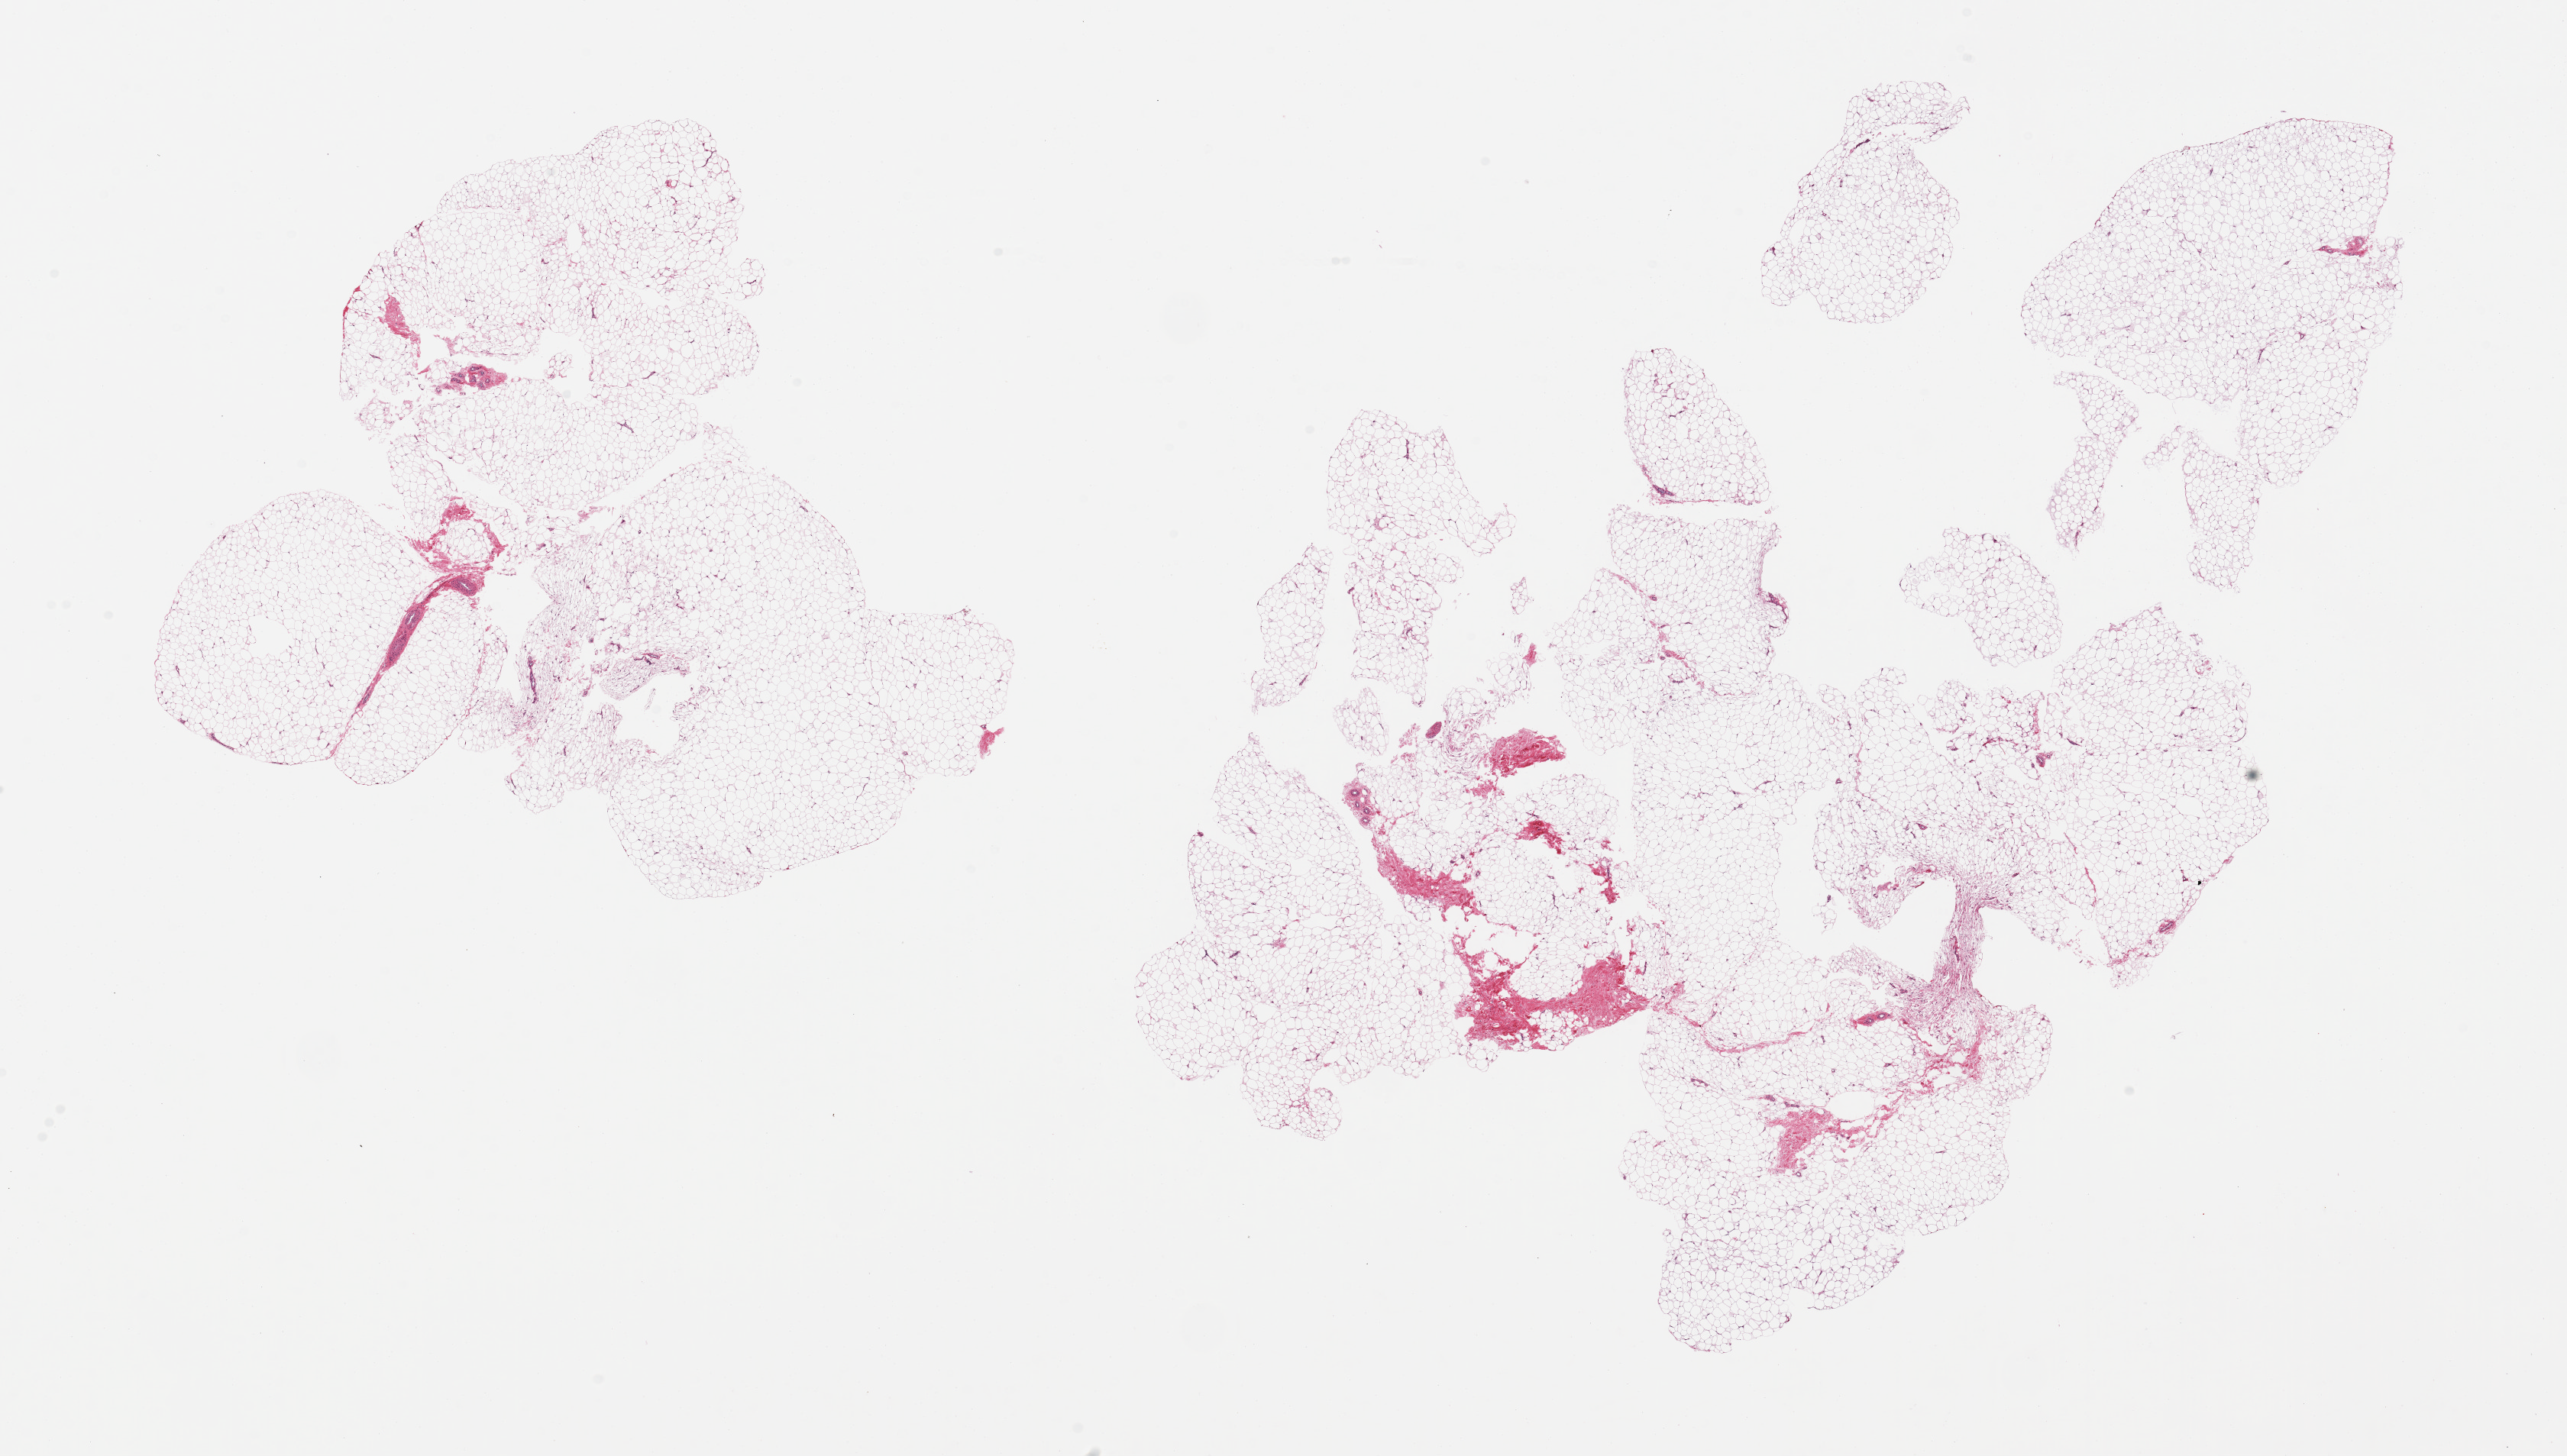
Digitized haematoxylin and eosin-stained section, brightfield — shown as a low-resolution overview of the whole scanned area (about 26.6 x 15.1 mm); PAXgene-fixed, paraffin-embedded tissue; section of adipose tissue (target tissue); tissue donor sample. Donor sex: male.
Pathologist's review note for this sample: 2 pieces; mature fat.